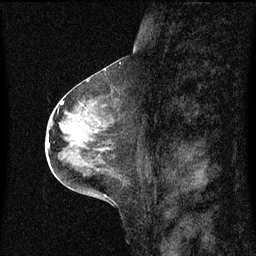
Breast MRI (dynamic contrast-enhanced), one sagittal slice. Position 32 of 60 along the scan axis. Dynamic contrast-enhanced series, image 2 of 3 at this slice position (ordered by acquisition). 1.5 T. TE 4.2 ms, TR 8.4 ms. 256 × 256 image matrix, field of view 200 × 200 mm. Patient: female, 49 years. From the clinical record (not read from this slice): setting: breast cancer imaged before/during neoadjuvant chemotherapy; receptor status: HR-positive, HER2-negative.
Structures marked on this image (semi-automatically segmented with operator editing):
- analysis volume of interest (the breast-tissue region the enhancement analysis was run in; not a lesion): bounding box (x1, y1, x2, y2) in pixels: (59, 101, 115, 158)
- tumour enhancement mask (voxels above the 70 % enhancement threshold inside the analysis volume of interest): (63, 128, 81, 139)